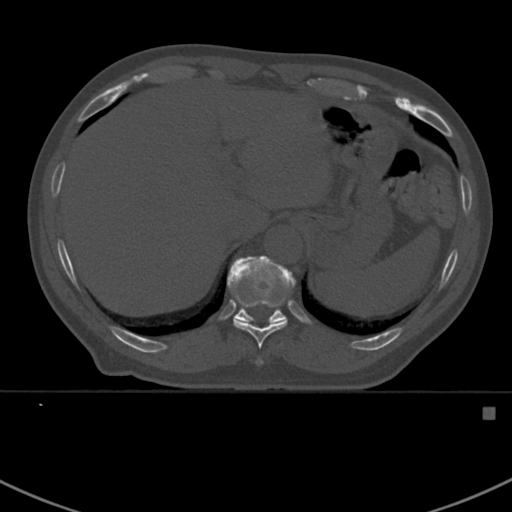
CT including the spine, one axial slice; slice 360 of 412 in the series (ordered by position); bone window (W 1800 / L 400 HU); 1.5 mm slice thickness; 512 × 512 image matrix. Male patient, age 59 years. Case-level facts recorded for this patient, not image findings: primary cancer: prostate.
Outlined on this slice (semi-automatic segmentation, software-assisted and operator-edited):
- T10 vertebra: box from (x=232, y=293) to (x=287, y=365) px
- T11 vertebra: (x=227, y=256)–(x=295, y=324)